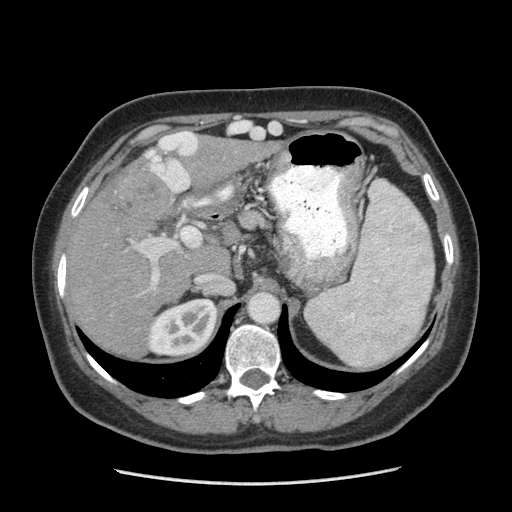
Contrast-enhanced abdominal CT (liver protocol), one axial slice; position 155 of 185 along the scan axis; 140 kVp; soft-tissue window (W 400 / L 40 HU); 2.5 mm slice thickness; 512 × 512 image matrix, field of view 360 × 360 mm. Case-level facts recorded for this patient, not image findings: diagnosis: hepatocellular carcinoma (patient treated with transarterial chemoembolisation; whether this scan precedes or follows treatment is not stated here); TNM stage (as recorded): Stage-I; Child-Pugh class: A.
Structures marked on this image (semi-automatically segmented with operator editing):
- liver parenchyma outside the tumour (the mass and vessels are separate outlines, so this box may not span the whole liver): bounding box <66,135,261,356> (left, top, right, bottom; pixels)
- mass: <111,164,171,222>
- liver vessels: <139,238,177,289>